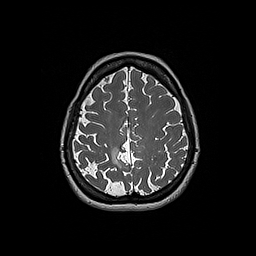
Brain MRI from a brain-tumour surgery series, one axial slice. Slice 57 of 192 in the series (ordered by position). 1 mm slice thickness. 256 × 256 image matrix. Case-level facts recorded for this patient, not image findings: histopathology: Oligodendroglioma; WHO grade: 2; IDH mutation: yes.
Outlined on this slice (expert manual segmentation):
- tumour: bounding box [x1, y1, x2, y2] px = [111, 146, 121, 168]